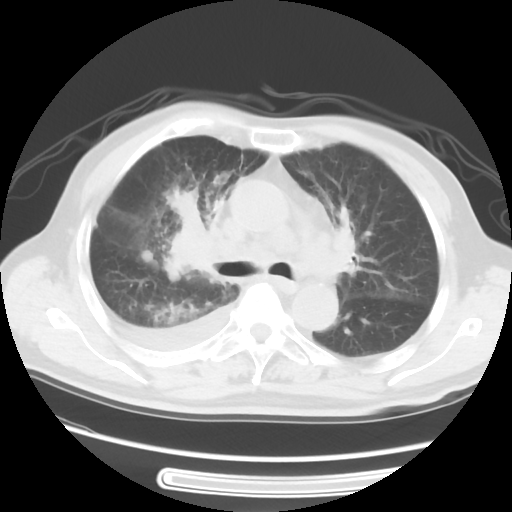
Chest CT, one axial slice. Reconstruction kernel STANDARD. 120 kVp. Lung window (W 1500 / L -600 HU). 5 mm slice thickness. 512 × 512 image matrix, field of view 360 × 360 mm. Male patient, age 77 years. From the clinical record (not read from this slice): clinical TNM (as recorded): T3 N3 M1b; histopathological grade: G3.
Structures marked on this image (rectangle marked by the reading radiologist):
- lung tumour (recorded histology: small cell carcinoma): bounding box <157,195,231,281> (left, top, right, bottom; pixels)